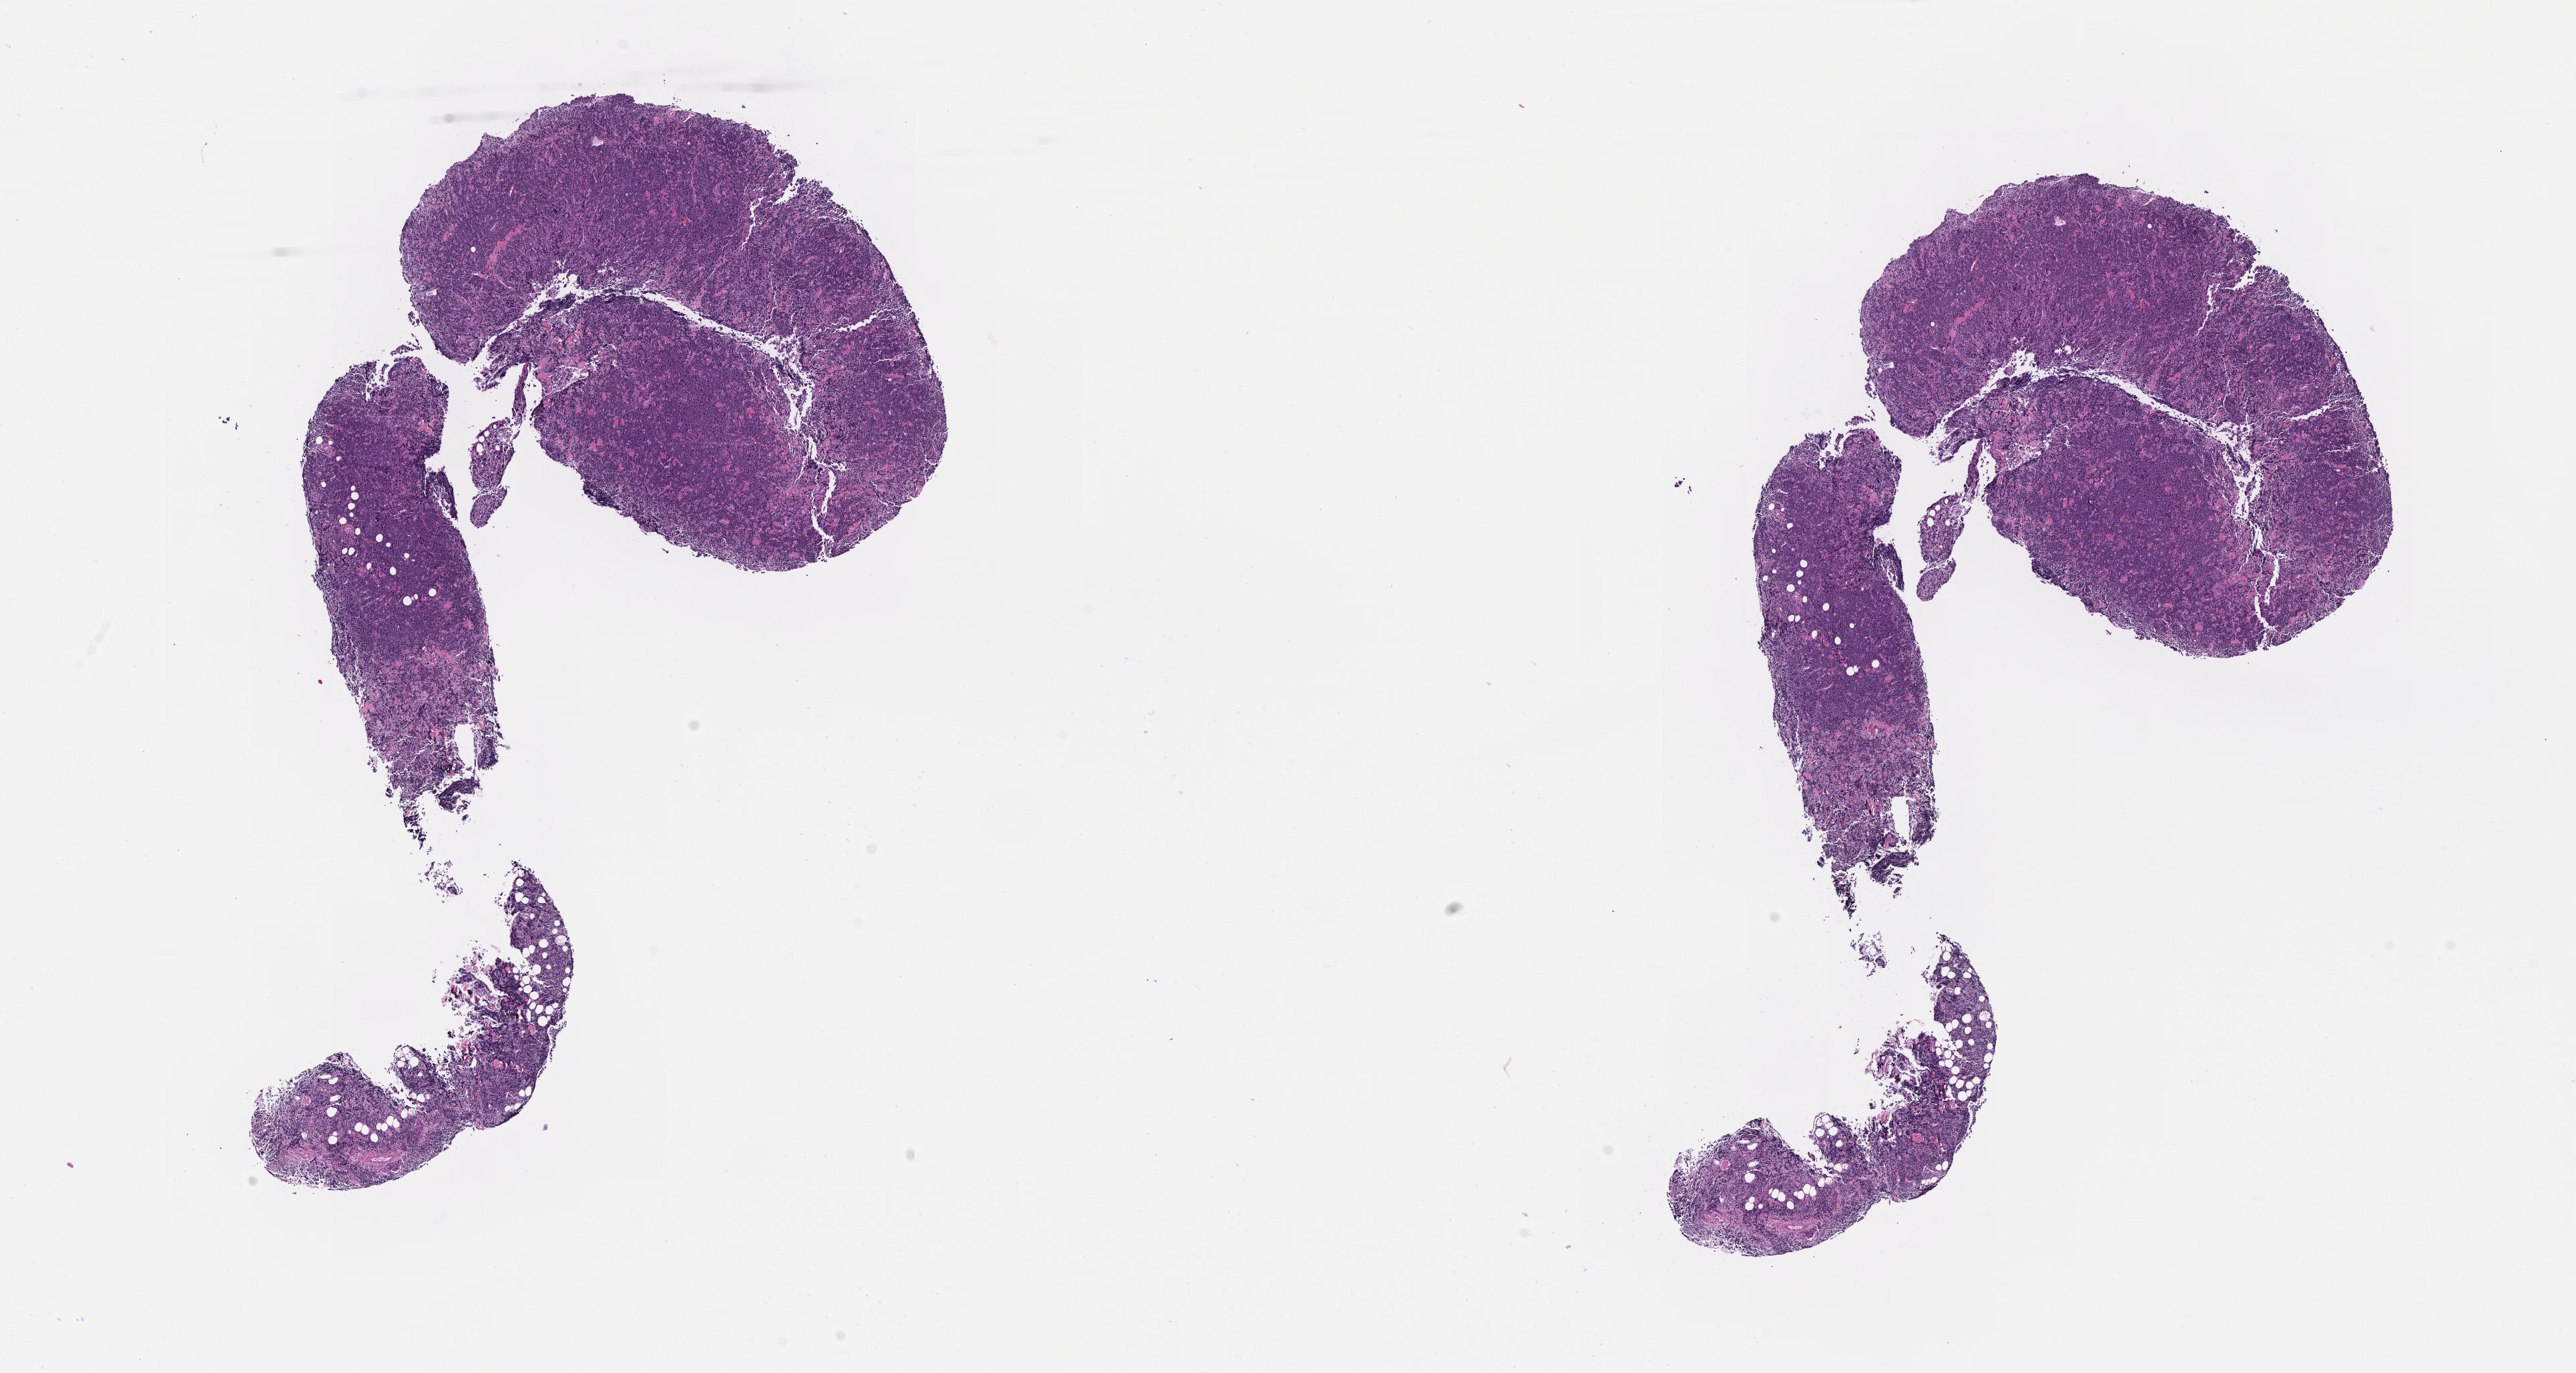
Whole-slide image, H&E stain, a low-resolution overview of the entire scanned area, about 15.6 x 8.3 mm; specimen: tumor tissue; site: head and neck. Female patient, aged 55.
Diagnosis: Burkitt lymphoma, NOS.